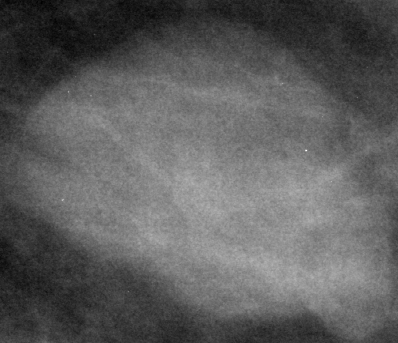
Cropped region of a digitized screen-film mammogram centred on a radiologist-marked abnormality; left breast; MLO view; BI-RADS breast density category 2 (scale 1–4).
Finding: mass, shape lobulated, margins circumscribed; BI-RADS assessment category 3; subtlety rating 5 on a 1 (subtle) to 5 (obvious) scale; pathology result (as recorded, not read from the image): benign.